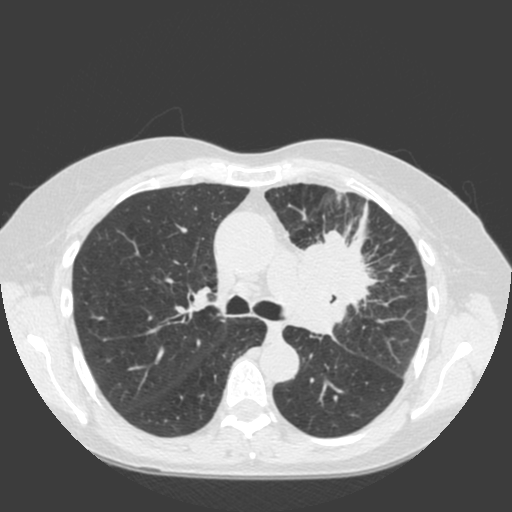
Low-dose screening chest CT, one axial slice. Position 123 of 184 along the scan axis. 120 kVp. Lung window (W 1500 / L -600 HU). 2 mm slice thickness. 512 × 512 image matrix, field of view 350 × 350 mm.
Structures marked on this image (manually delineated by an expert):
- lesion 1 (tumor, hilum of left lung): box from (x=287, y=204) to (x=378, y=336) px